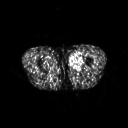
FDG PET of an extremity soft-tissue mass (from a PET/CT study), one axial slice; slice 243 of 311 in the series (ordered by position); 128 × 128 image matrix. Patient: male, 29 years. Case-level facts recorded for this patient, not image findings: histological type: mixoid liposarcoma; grade: low; site of the primary tumour: left thigh.
Annotated regions visible in this slice (expert contour drawn on MRI and transferred to this co-registered scan by the dataset authors):
- gross tumour volume (mass): box from (x=69, y=53) to (x=82, y=69) px